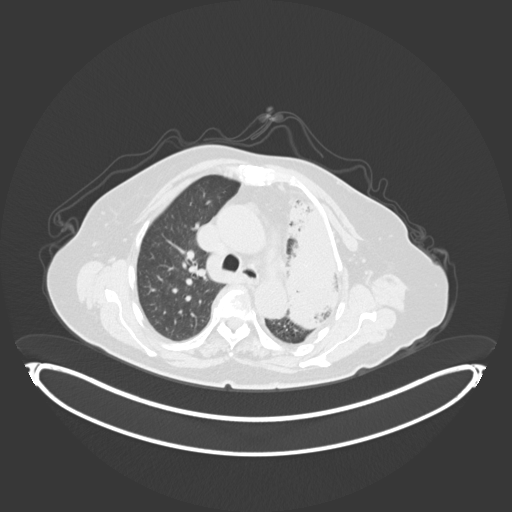
Chest CT, one axial slice; position 214 of 284 along the scan axis; lung window (W 1500 / L -600 HU); 3 mm slice thickness; 512 × 512 image matrix, field of view 500 × 500 mm. Patient: female, 75 years. Case-level facts recorded for this patient, not image findings: clinical TNM (as recorded): T3 N3 M1.
Annotated regions visible in this slice (bounding box drawn by a radiologist):
- lung tumour (recorded histology: adenocarcinoma): bounding box (x1, y1, x2, y2) in pixels: (282, 193, 346, 336)